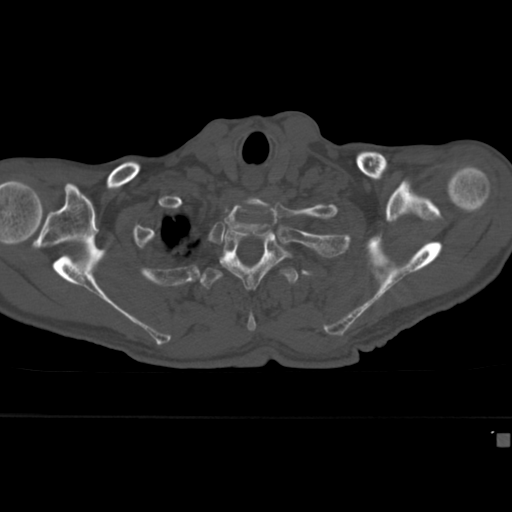
CT including the spine, one axial slice; slice 343 of 430 in the series (ordered by position); 120 kVp; bone window (W 1800 / L 400 HU); 512 × 512 image matrix, field of view 337 × 337 mm. Patient: male, 64 years. Case-level facts recorded for this patient, not image findings: primary cancer: uterus.
Outlined on this slice (semi-automatically segmented with operator editing):
- T2 vertebra: box from (x=219, y=230) to (x=292, y=290) px
- T3 vertebra: (x=199, y=263)–(x=299, y=332)